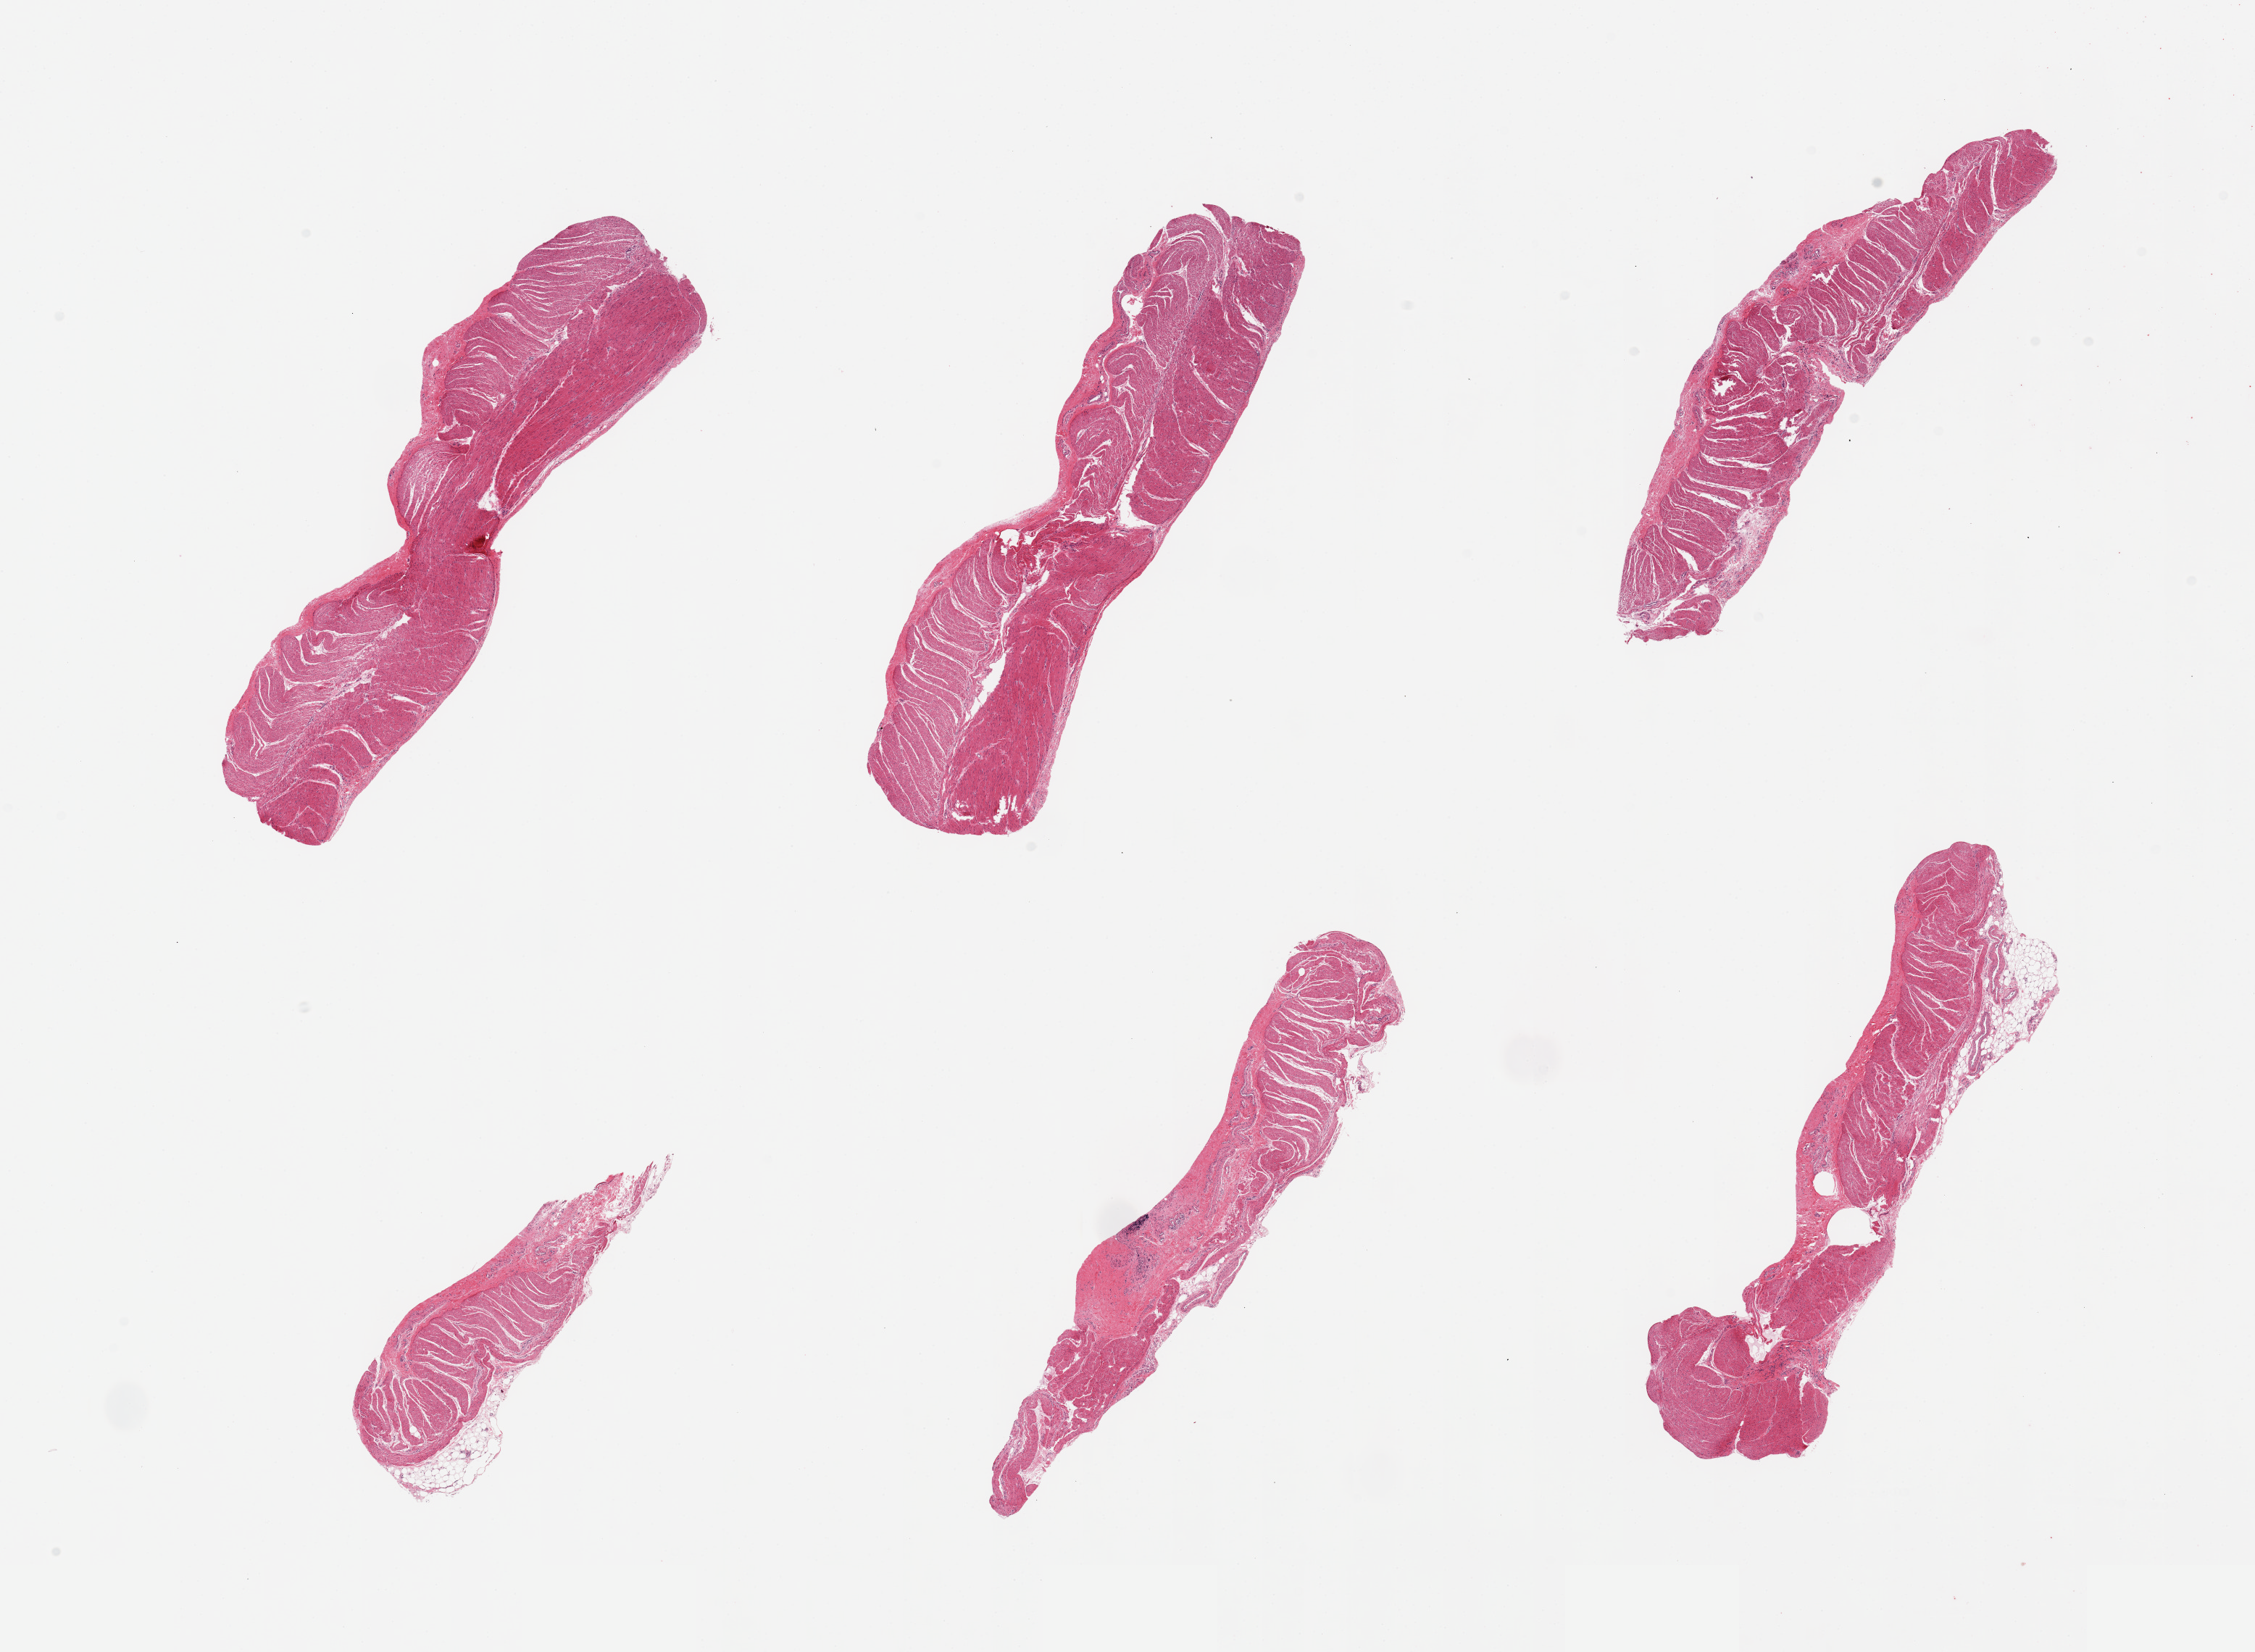
Digitized haematoxylin and eosin-stained section, brightfield — a low-resolution overview of the entire scanned area, about 24.6 x 18.0 mm (slide scanned at 20x). PAXgene-fixed paraffin-embedded (PFPE) section. Section of sigmoid colon (target tissue). Donor tissue sample.
Reviewer comment on this tissue sample: 6 pieces; well dissected muscle.